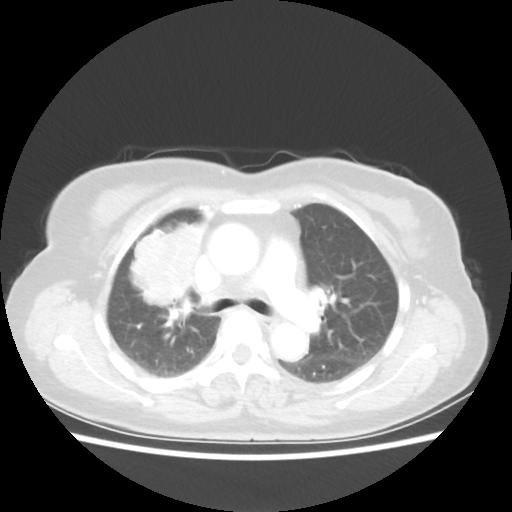
Chest CT, one axial slice. Position 35 of 55 along the scan axis. Lung window (W 1500 / L -600 HU). 512 × 512 image matrix, field of view 337 × 337 mm. Patient: female, 62 years. Case-level facts recorded for this patient, not image findings: clinical TNM (as recorded): T4 N3 M0.
Structures marked on this image (bounding box drawn by a radiologist):
- lung tumour (recorded histology: squamous cell carcinoma): bounding box <129,218,213,316> (left, top, right, bottom; pixels)